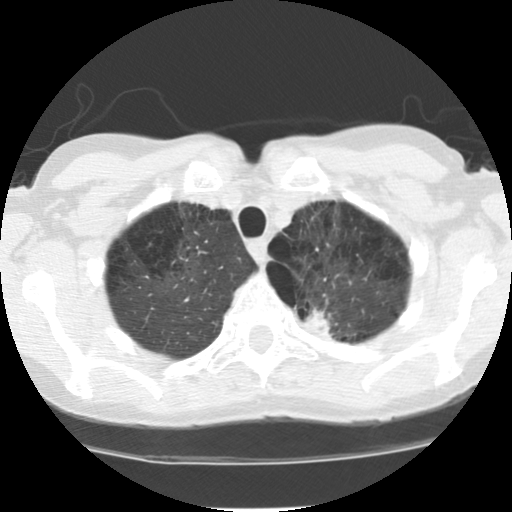
Chest CT (low-dose screening protocol), one axial image. First (baseline) screen. Lung window (W 1500 / L -600 HU). 120 kVp. 512 × 512 image matrix, field of view 300 × 300 mm. Female participant, aged 61 years at enrolment. Current smoker at enrolment.
Expert reader's lesion annotation, bounding box (x1, y1, x2, y2) in pixels: (293, 294, 350, 346). The screening reader recorded 4 non-calcified nodules or masses ≥4 mm on this exam (left upper lobe, right lower lobe, right middle lobe, left lower lobe); which of them this box marks is not recorded. Lung cancer was diagnosed 68 days after this screen: adenocarcinoma, NOS, left upper lobe, poorly differentiated (G3), stage IB (AJCC 6th edition), 17 mm at pathology.